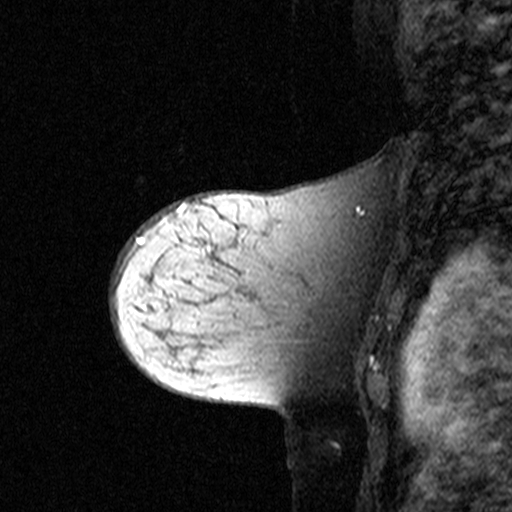
Breast MRI (dynamic contrast-enhanced), one sagittal slice; position 30 of 44 along the scan axis; dynamic contrast-enhanced study with each time point stored as its own series, time point 2 of 3 at this slice position (early post-contrast, ordered by acquisition time); 1.5 T; TE 4.5 ms, TR 11 ms; 3 mm slice thickness; 512 × 512 image matrix, field of view 200 × 200 mm. Female patient, age 44 years. From the clinical record (not read from this slice): setting: breast cancer imaged before/during neoadjuvant chemotherapy; receptor status: triple-negative.
Outlined on this slice (semi-automatic segmentation, software-assisted and operator-edited):
- analysis volume of interest (the breast-tissue region the enhancement analysis was run in; not a lesion): bounding box (x1, y1, x2, y2) in pixels: (142, 208, 349, 363)
- tumour enhancement mask (voxels above the 90 % enhancement threshold inside the analysis volume of interest): (142, 208, 209, 249)